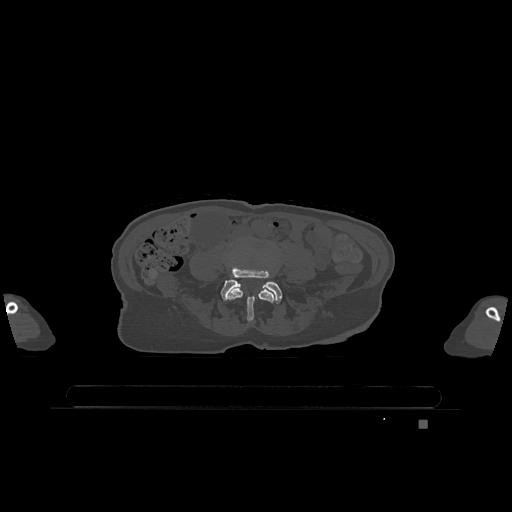
CT including the spine, one axial slice; position 267 of 1317 along the scan axis; bone window (W 1800 / L 400 HU); 512 × 512 image matrix, field of view 500 × 500 mm. Female patient, age 74 years. From the clinical record (not read from this slice): primary cancer: lung.
Structures marked on this image (semi-automatically segmented with operator editing):
- L4 vertebra: bounding box (x1, y1, x2, y2) in pixels: (228, 288, 274, 322)
- L5 vertebra: (221, 268, 282, 304)